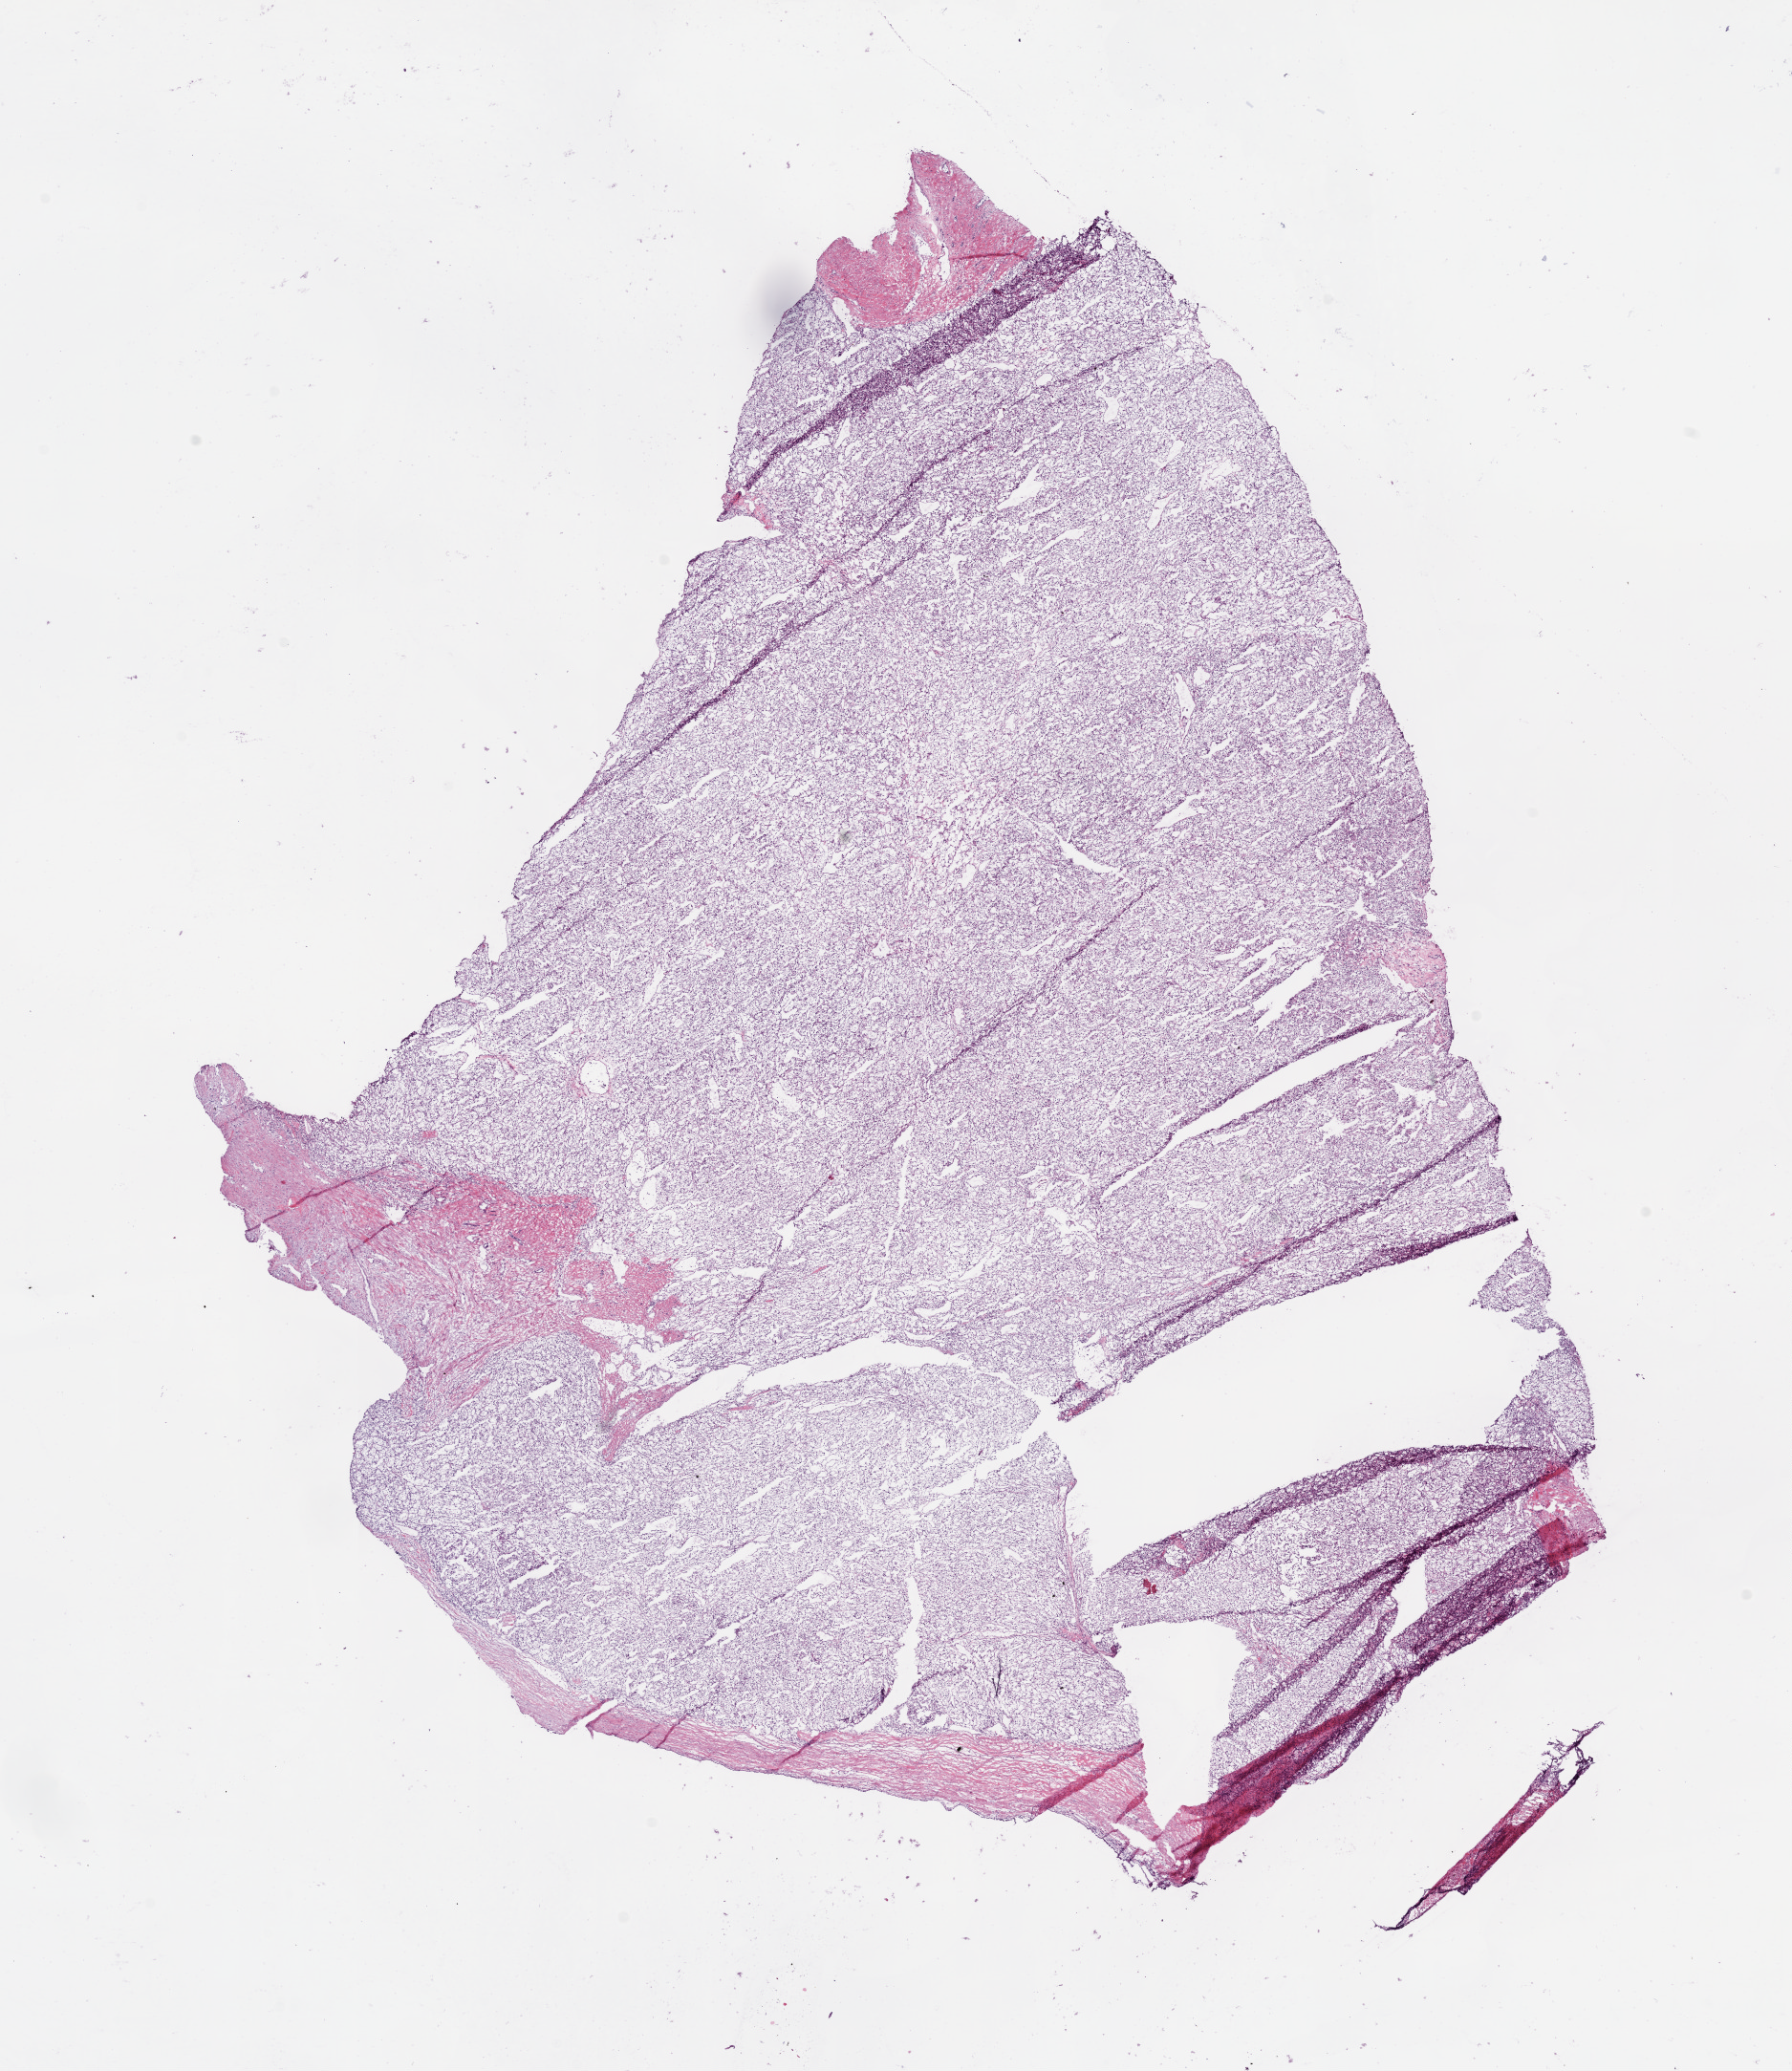
Hematoxylin and eosin (H&E) stained whole-slide image, shown as a low-resolution overview of the whole scanned area (about 15.0 x 17.4 mm, from a 20x scan). Frozen section from the bottom of the tissue portion. Sample: primary tumour, kidney. Male, age 75 years at initial diagnosis. Histologic grade: G2 (moderately differentiated). Composition of this section per pathologist review: tumour cells 90%, tumour nuclei 90%, normal cells 0%, stromal cells 10%, necrosis 0%.
AJCC pathologic stage: III. Laterality: right. Pathologic diagnosis: Clear cell adenocarcinoma, NOS.